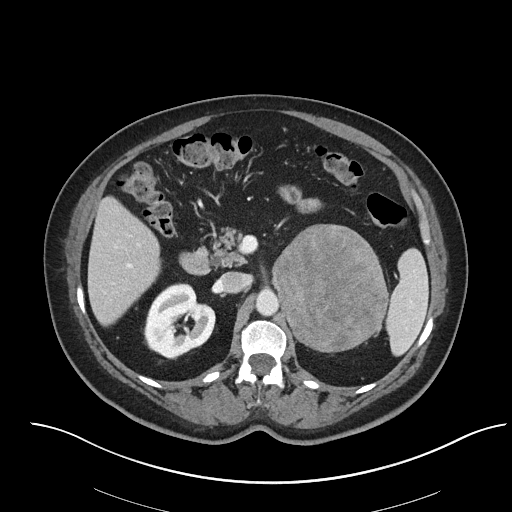
Contrast-enhanced abdominal CT, one axial slice. Reconstruction kernel I40f/2. 120 kVp. Intravenous contrast given. Soft-tissue window (W 400 / L 40 HU). 3 mm slice thickness. 512 × 512 image matrix, field of view 440 × 440 mm. Patient: female, 53 years. Case-level facts recorded for this patient, not image findings: diagnosis: adrenocortical carcinoma; tumour side: left adrenal; tumour size at pathology: 9 cm; Ki-67 index: 28 %; stage (as recorded): 2.
Outlined on this slice (semi-automatic segmentation, software-assisted and operator-edited):
- mass: box from (x=274, y=225) to (x=387, y=351) px